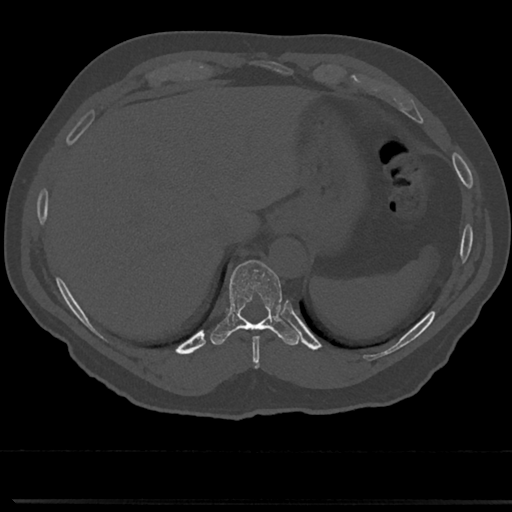
CT including the spine, one axial slice. Reconstruction kernel Br40s/3. 120 kVp. Bone window (W 1800 / L 400 HU). 0.5 mm slice thickness. 512 × 512 image matrix, field of view 355 × 355 mm. Male patient, age 61 years. From the clinical record (not read from this slice): primary cancer: prostate.
Structures marked on this image (semi-automatically segmented with operator editing):
- T10 vertebra: bounding box <229,261,283,325> (left, top, right, bottom; pixels)
- T9 vertebra: <246,323,276,354>